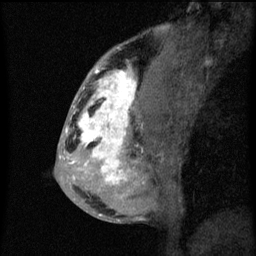
Breast MRI (dynamic contrast-enhanced), one sagittal slice. Dynamic contrast-enhanced series, image 2 of 3 at this slice position (ordered by acquisition). 1.5 T. TE 4.2 ms, TR 8 ms. 256 × 256 image matrix, field of view 180 × 180 mm. Patient: female, 50 years.
Annotated regions visible in this slice (semi-automatically segmented with operator editing):
- analysis volume of interest (the breast-tissue region the enhancement analysis was run in; not a lesion): bounding box (x1, y1, x2, y2) in pixels: (66, 64, 141, 187)
- tumour enhancement mask (voxels above the 70 % enhancement threshold inside the analysis volume of interest): (66, 66, 137, 185)